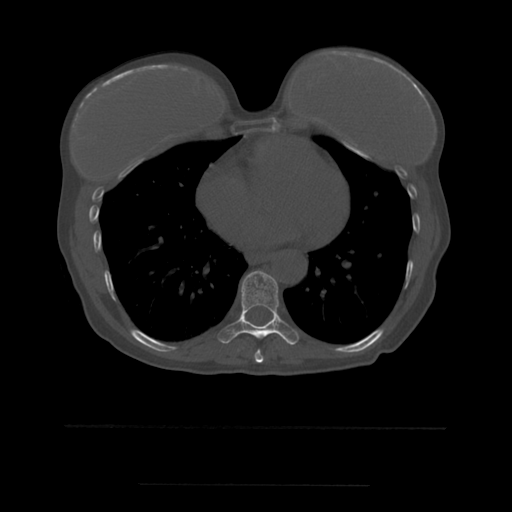
CT including the spine, one axial slice; position 323 of 544 along the scan axis; bone window (W 1800 / L 400 HU); 512 × 512 image matrix, field of view 350 × 350 mm. Patient age 58 years. From the clinical record (not read from this slice): primary cancer: lung.
Annotated regions visible in this slice (semi-automatically segmented with operator editing):
- T8 vertebra: bounding box [x1, y1, x2, y2] px = [255, 350, 264, 363]
- T9 vertebra: [220, 271, 300, 345]